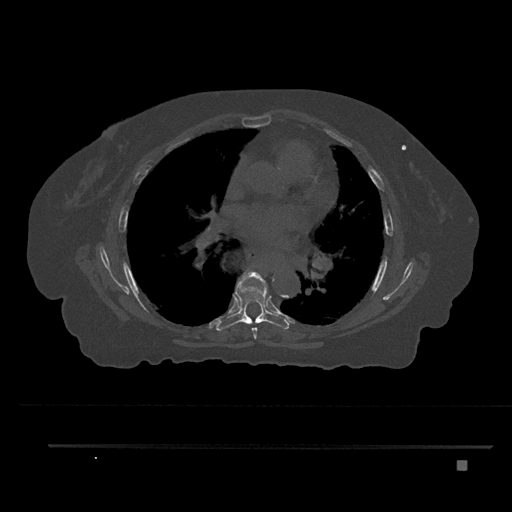
CT including the spine, one axial slice; bone window (W 1800 / L 400 HU); 0.5 mm slice thickness; 512 × 512 image matrix, field of view 437 × 437 mm. Female patient, age 76 years. From the clinical record (not read from this slice): primary cancer: lung; vertebrae with lytic lesions (as recorded): T11, L3.
Annotated regions visible in this slice (semi-automatic segmentation, software-assisted and operator-edited):
- T6 vertebra: bounding box <243,271,268,339> (left, top, right, bottom; pixels)
- T7 vertebra: <216,281,290,331>